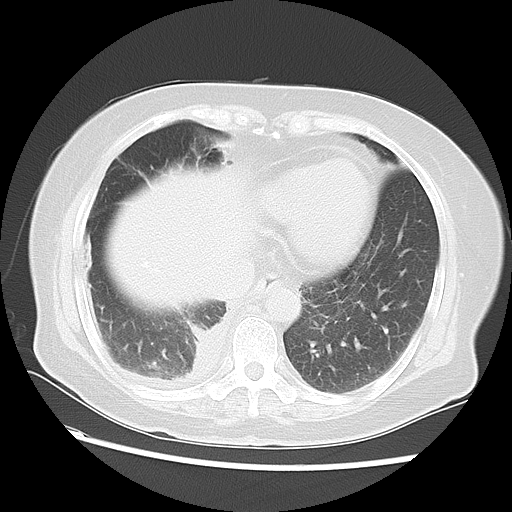
Chest CT, one axial slice; slice 20 of 57 in the series (ordered by position); reconstruction kernel LUNG; 120 kVp; lung window (W 1500 / L -600 HU); 512 × 512 image matrix. Female patient, age 69 years. Case-level facts recorded for this patient, not image findings: clinical TNM (as recorded): T2 N1 M1a.
Structures marked on this image (bounding box drawn by a radiologist):
- lung tumour (recorded histology: adenocarcinoma): bounding box <184,320,229,397> (left, top, right, bottom; pixels)